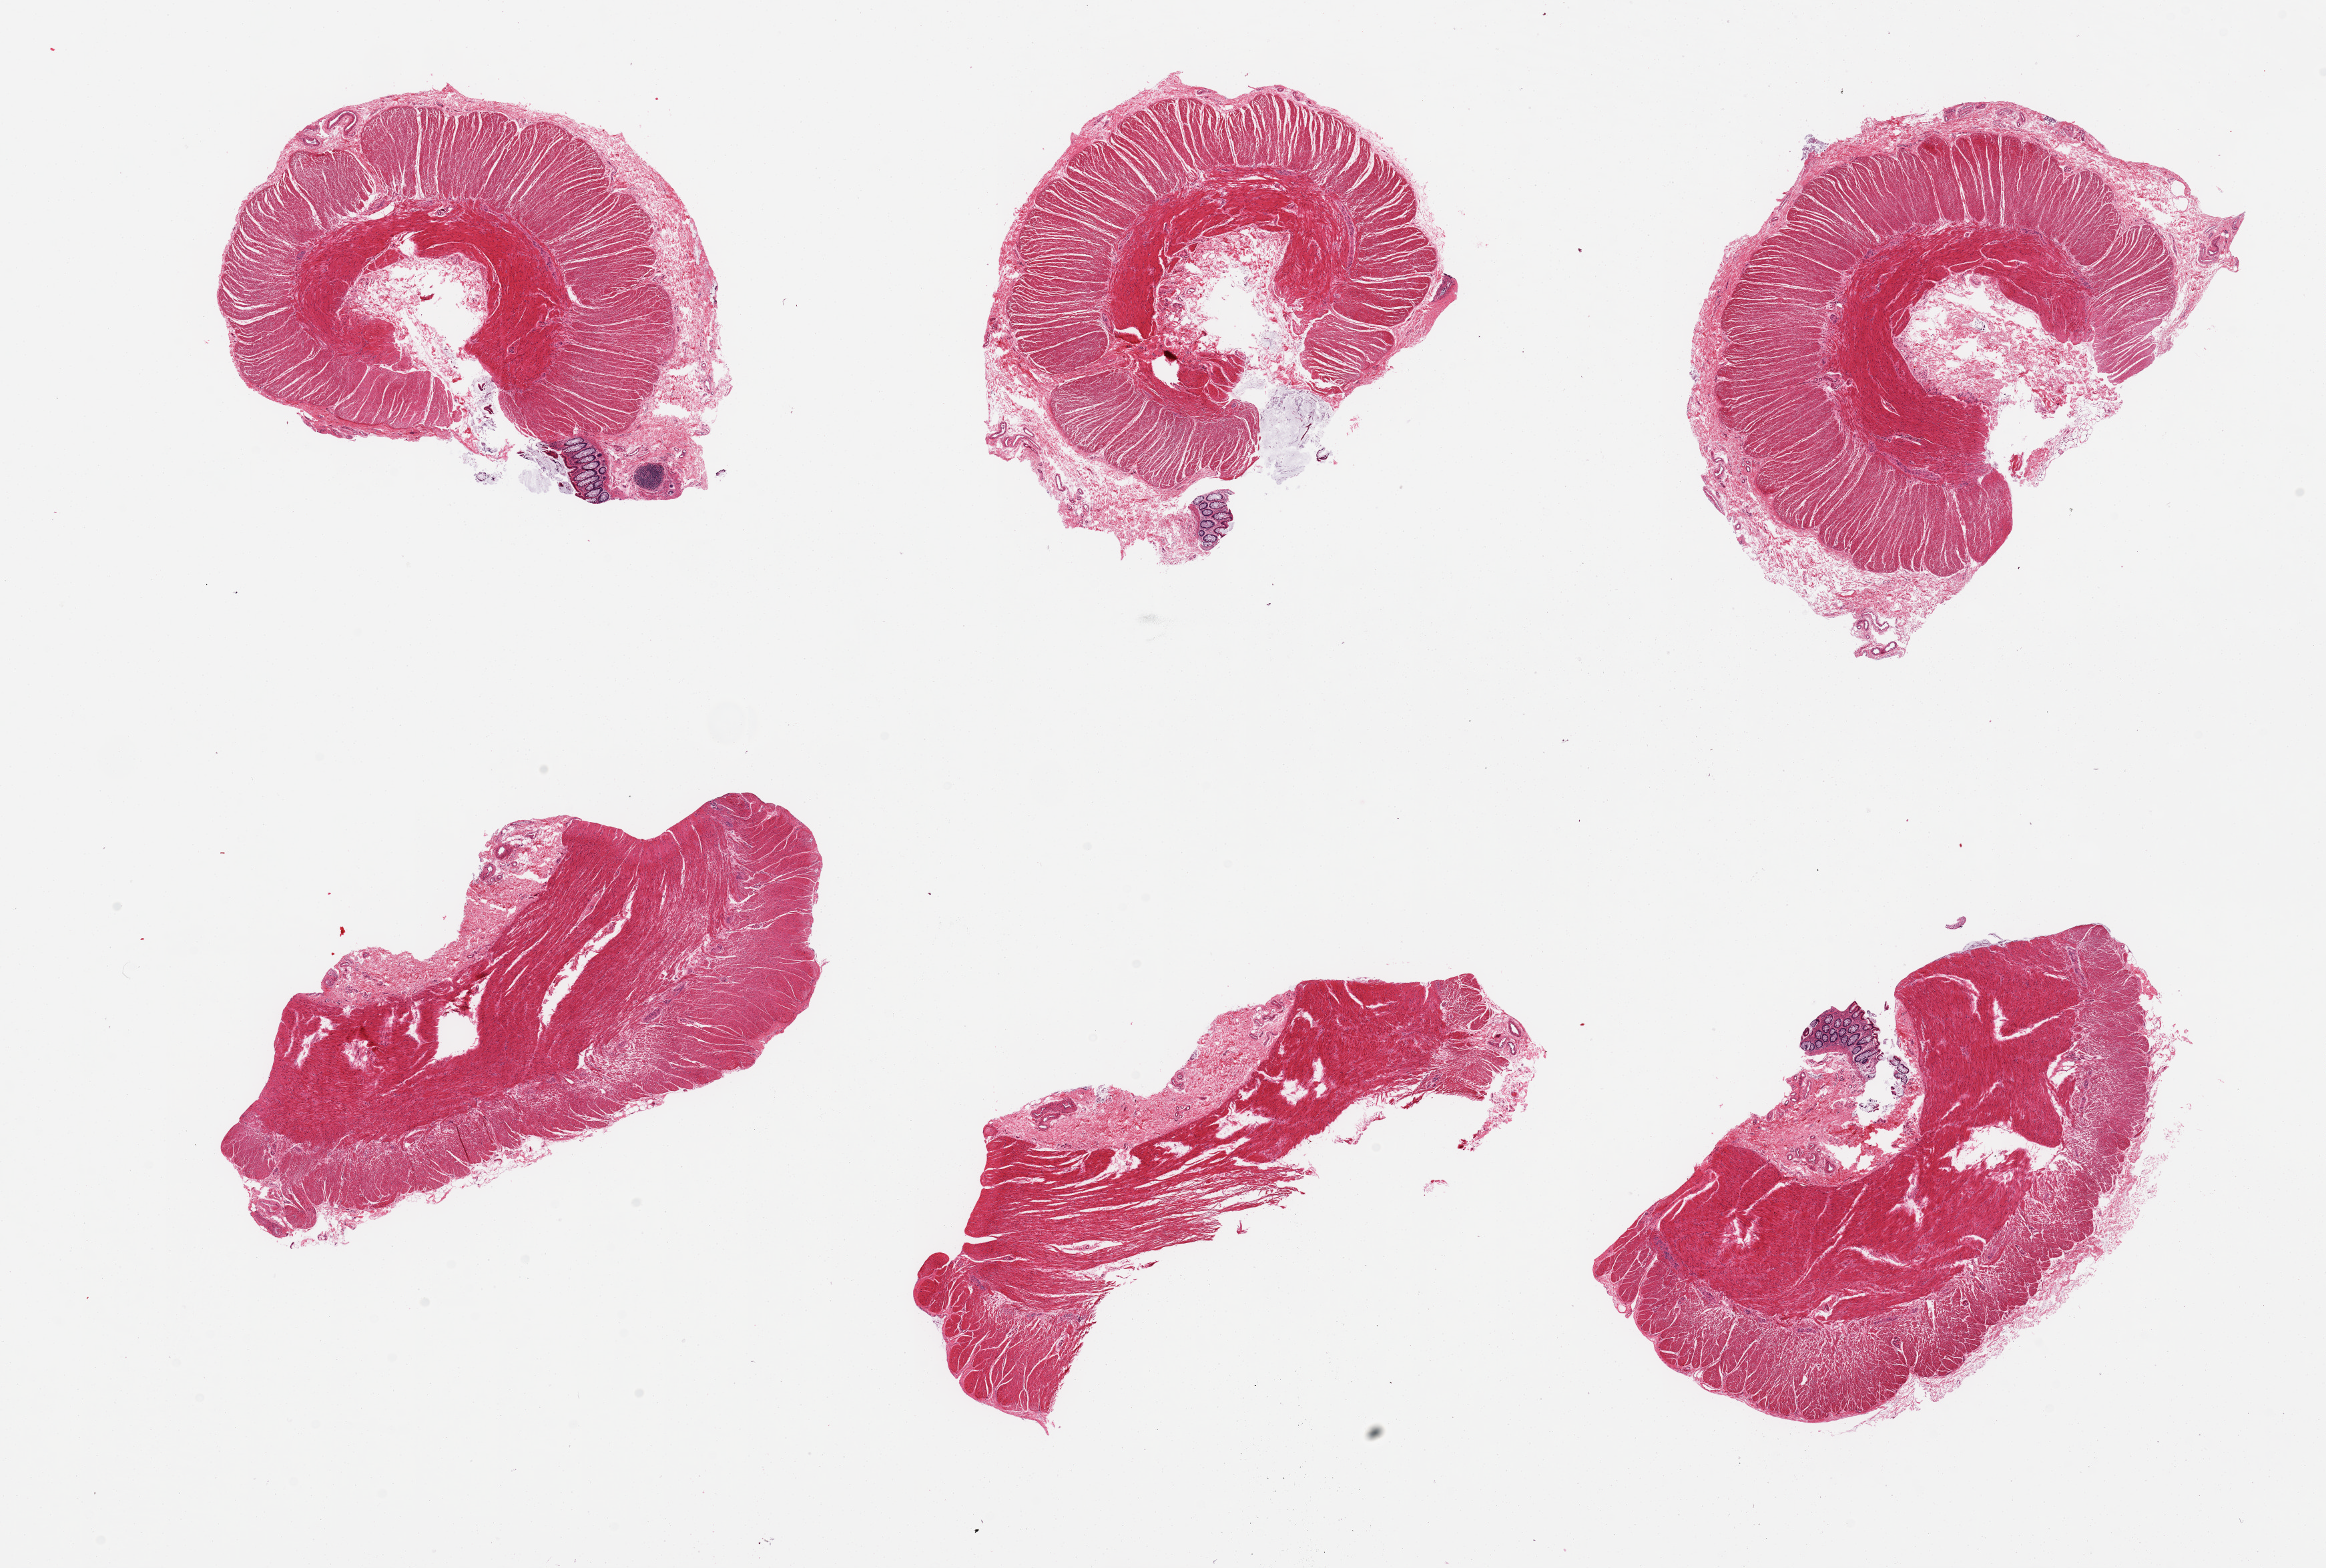
Digitized haematoxylin and eosin-stained section, brightfield — whole scanned area (about 27.6 x 18.6 mm, slide scanned at 20x) shown as a low-resolution overview. PAXgene-fixed paraffin-embedded (PFPE) section. Sampled site (target tissue): sigmoid colon. Tissue donor sample. Donor: male.
• reviewer comment on this tissue sample: 6 pieces, all muscularis, trace 'contaminant' mucosa; good specimens